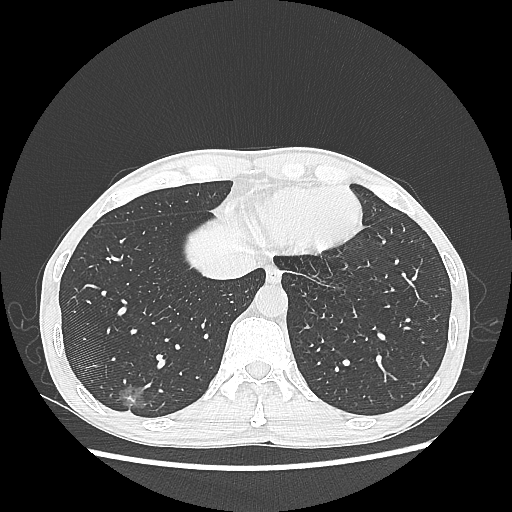
Chest CT, one axial slice. Position 69 of 270 along the scan axis. Lung window (W 1500 / L -600 HU). 1.25 mm slice thickness. 512 × 512 image matrix, field of view 360 × 360 mm. Male patient, age 60 years. Case-level facts recorded for this patient, not image findings: clinical TNM (as recorded): T1c N0 M0; histopathological grade: G2.
Annotated regions visible in this slice (rectangle marked by the reading radiologist):
- lung tumour (recorded histology: adenocarcinoma): bounding box <116,378,146,415> (left, top, right, bottom; pixels)